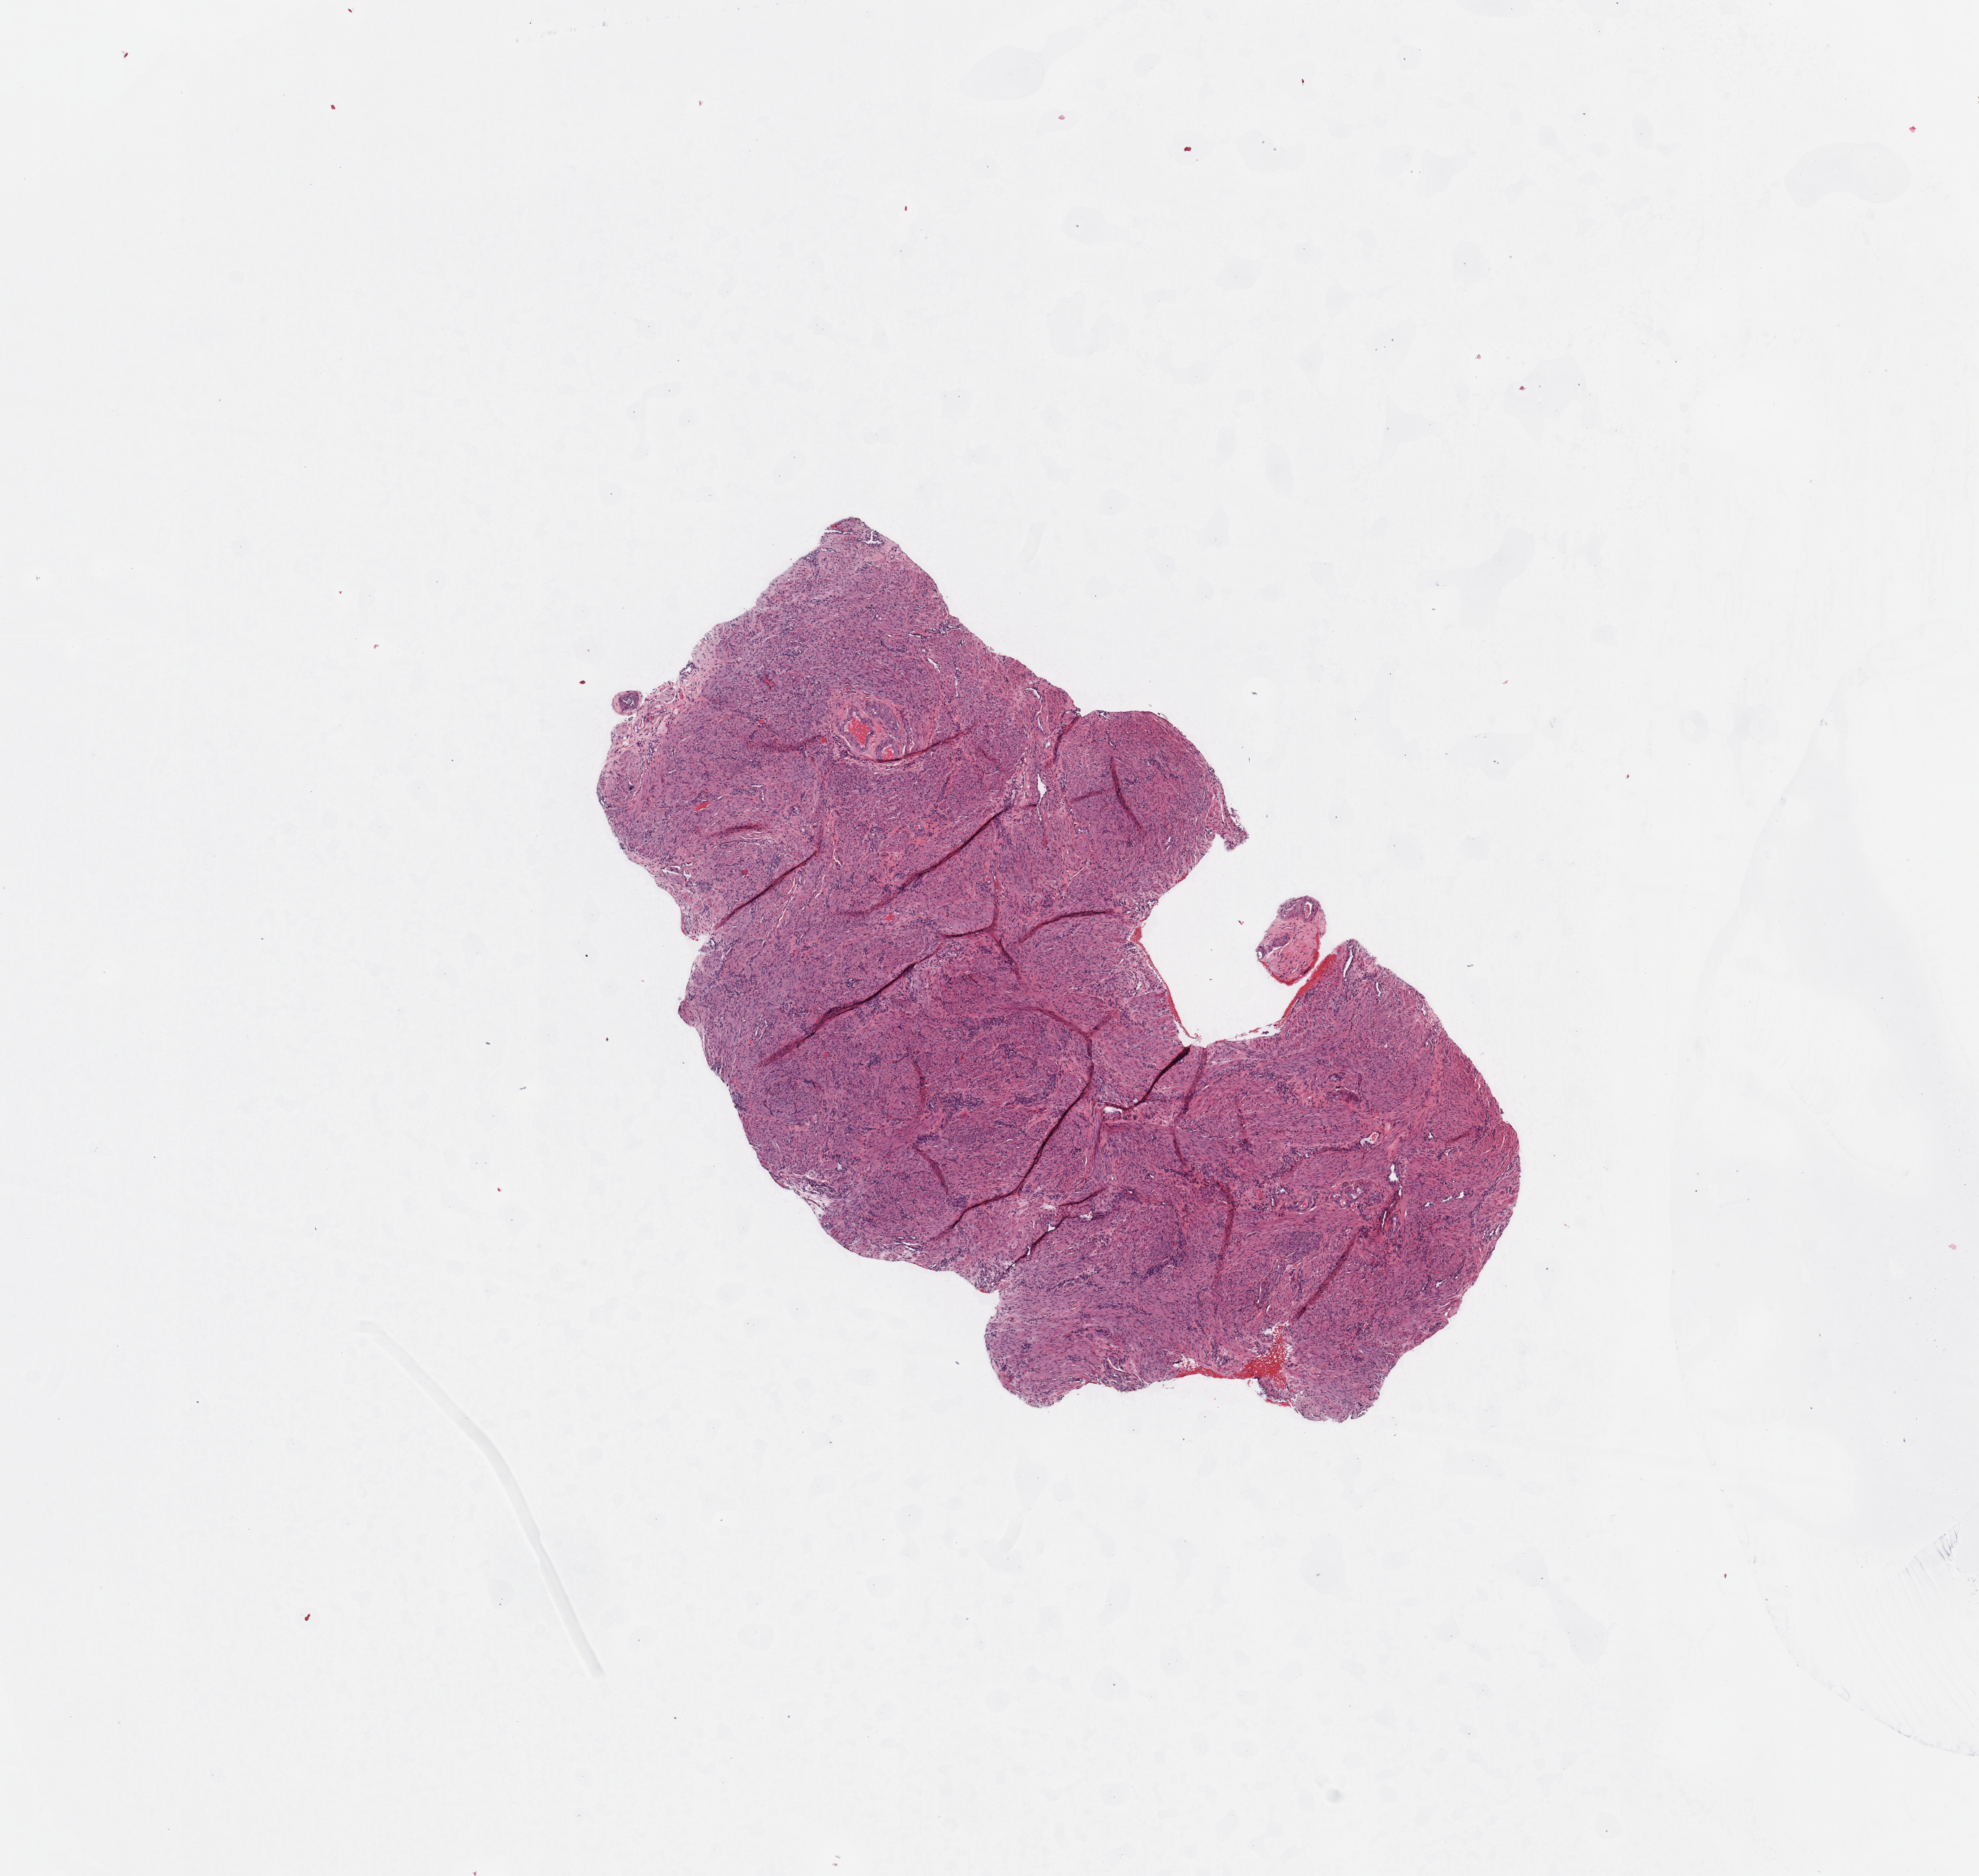
Whole-slide histology image, H&E, a low-resolution overview of the entire scanned area, about 10.8 x 10.3 mm (slide scanned at 20x); uterus, normal (non-tumour) tissue. 48-year-old female patient.
This section: normal (non-tumour) tissue from the same patient. Patient diagnosis: Endometrioid adenocarcinoma, NOS.